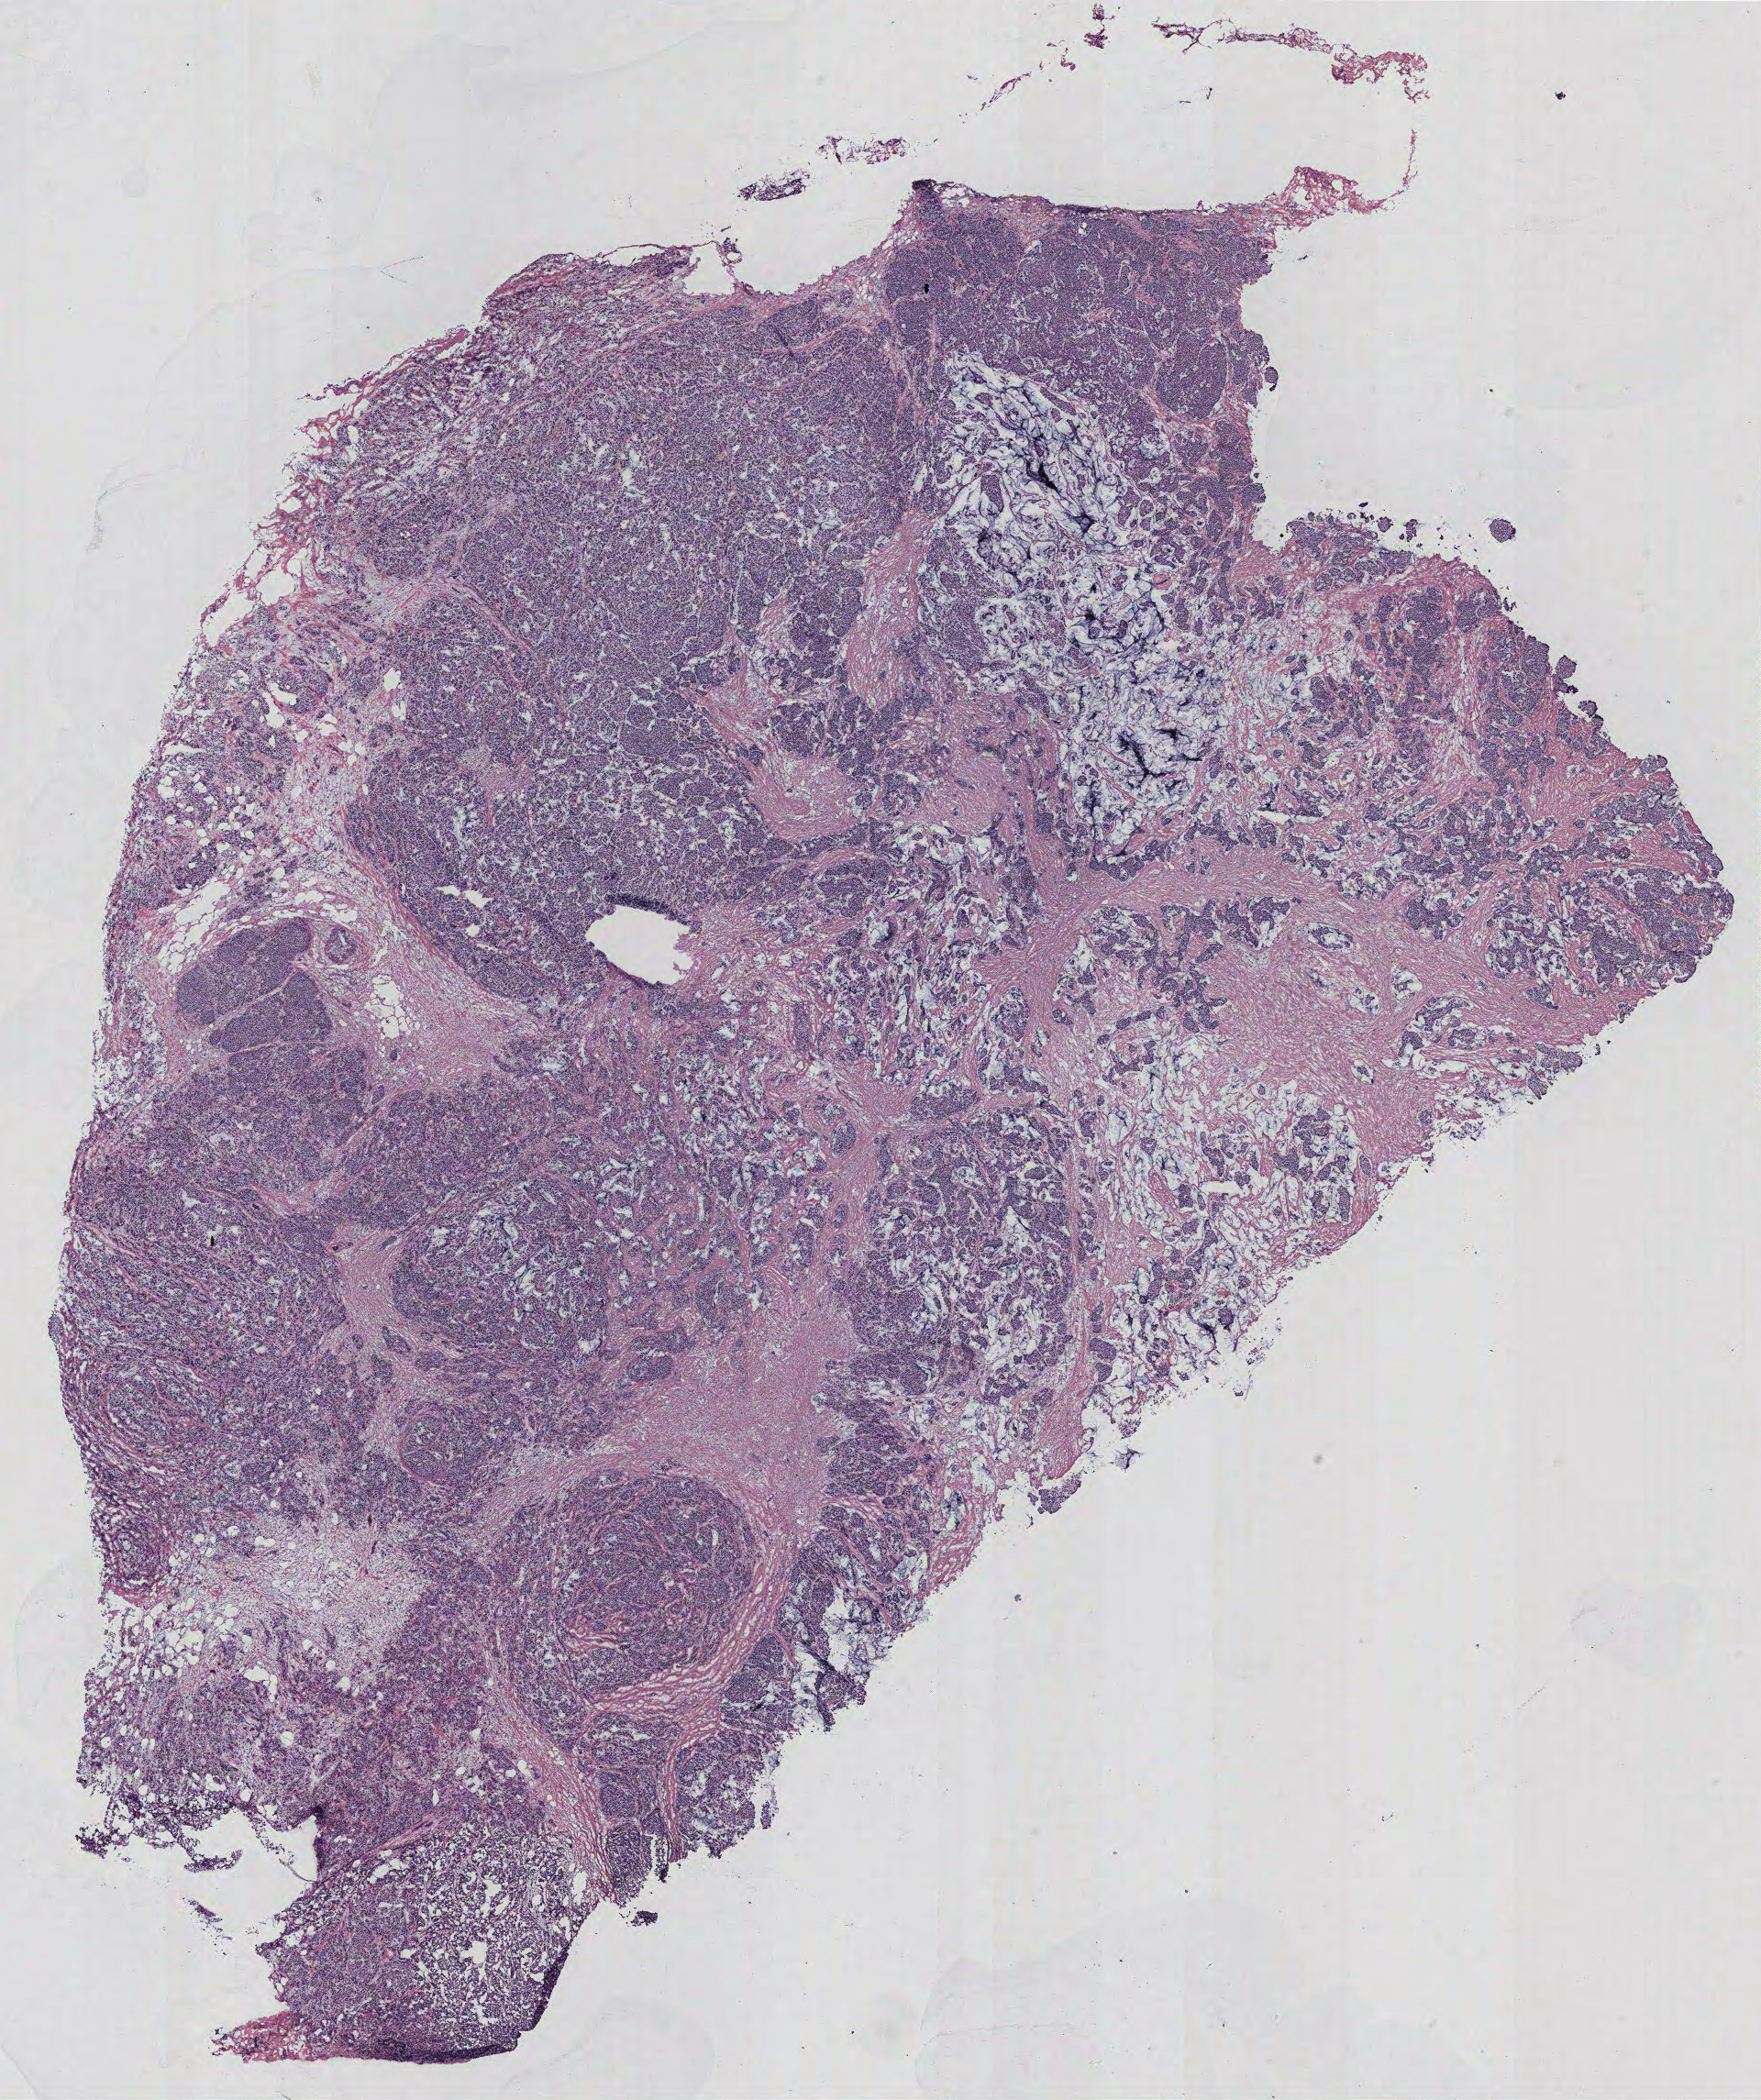
Whole-slide histology image, H&E-stained, a low-resolution overview of the entire scanned area, about 15.4 x 18.3 mm; breast, tissue type not recorded. Patient: female, age 76 years.
Patient diagnosis: Infiltrating duct and mucinous carcinoma.